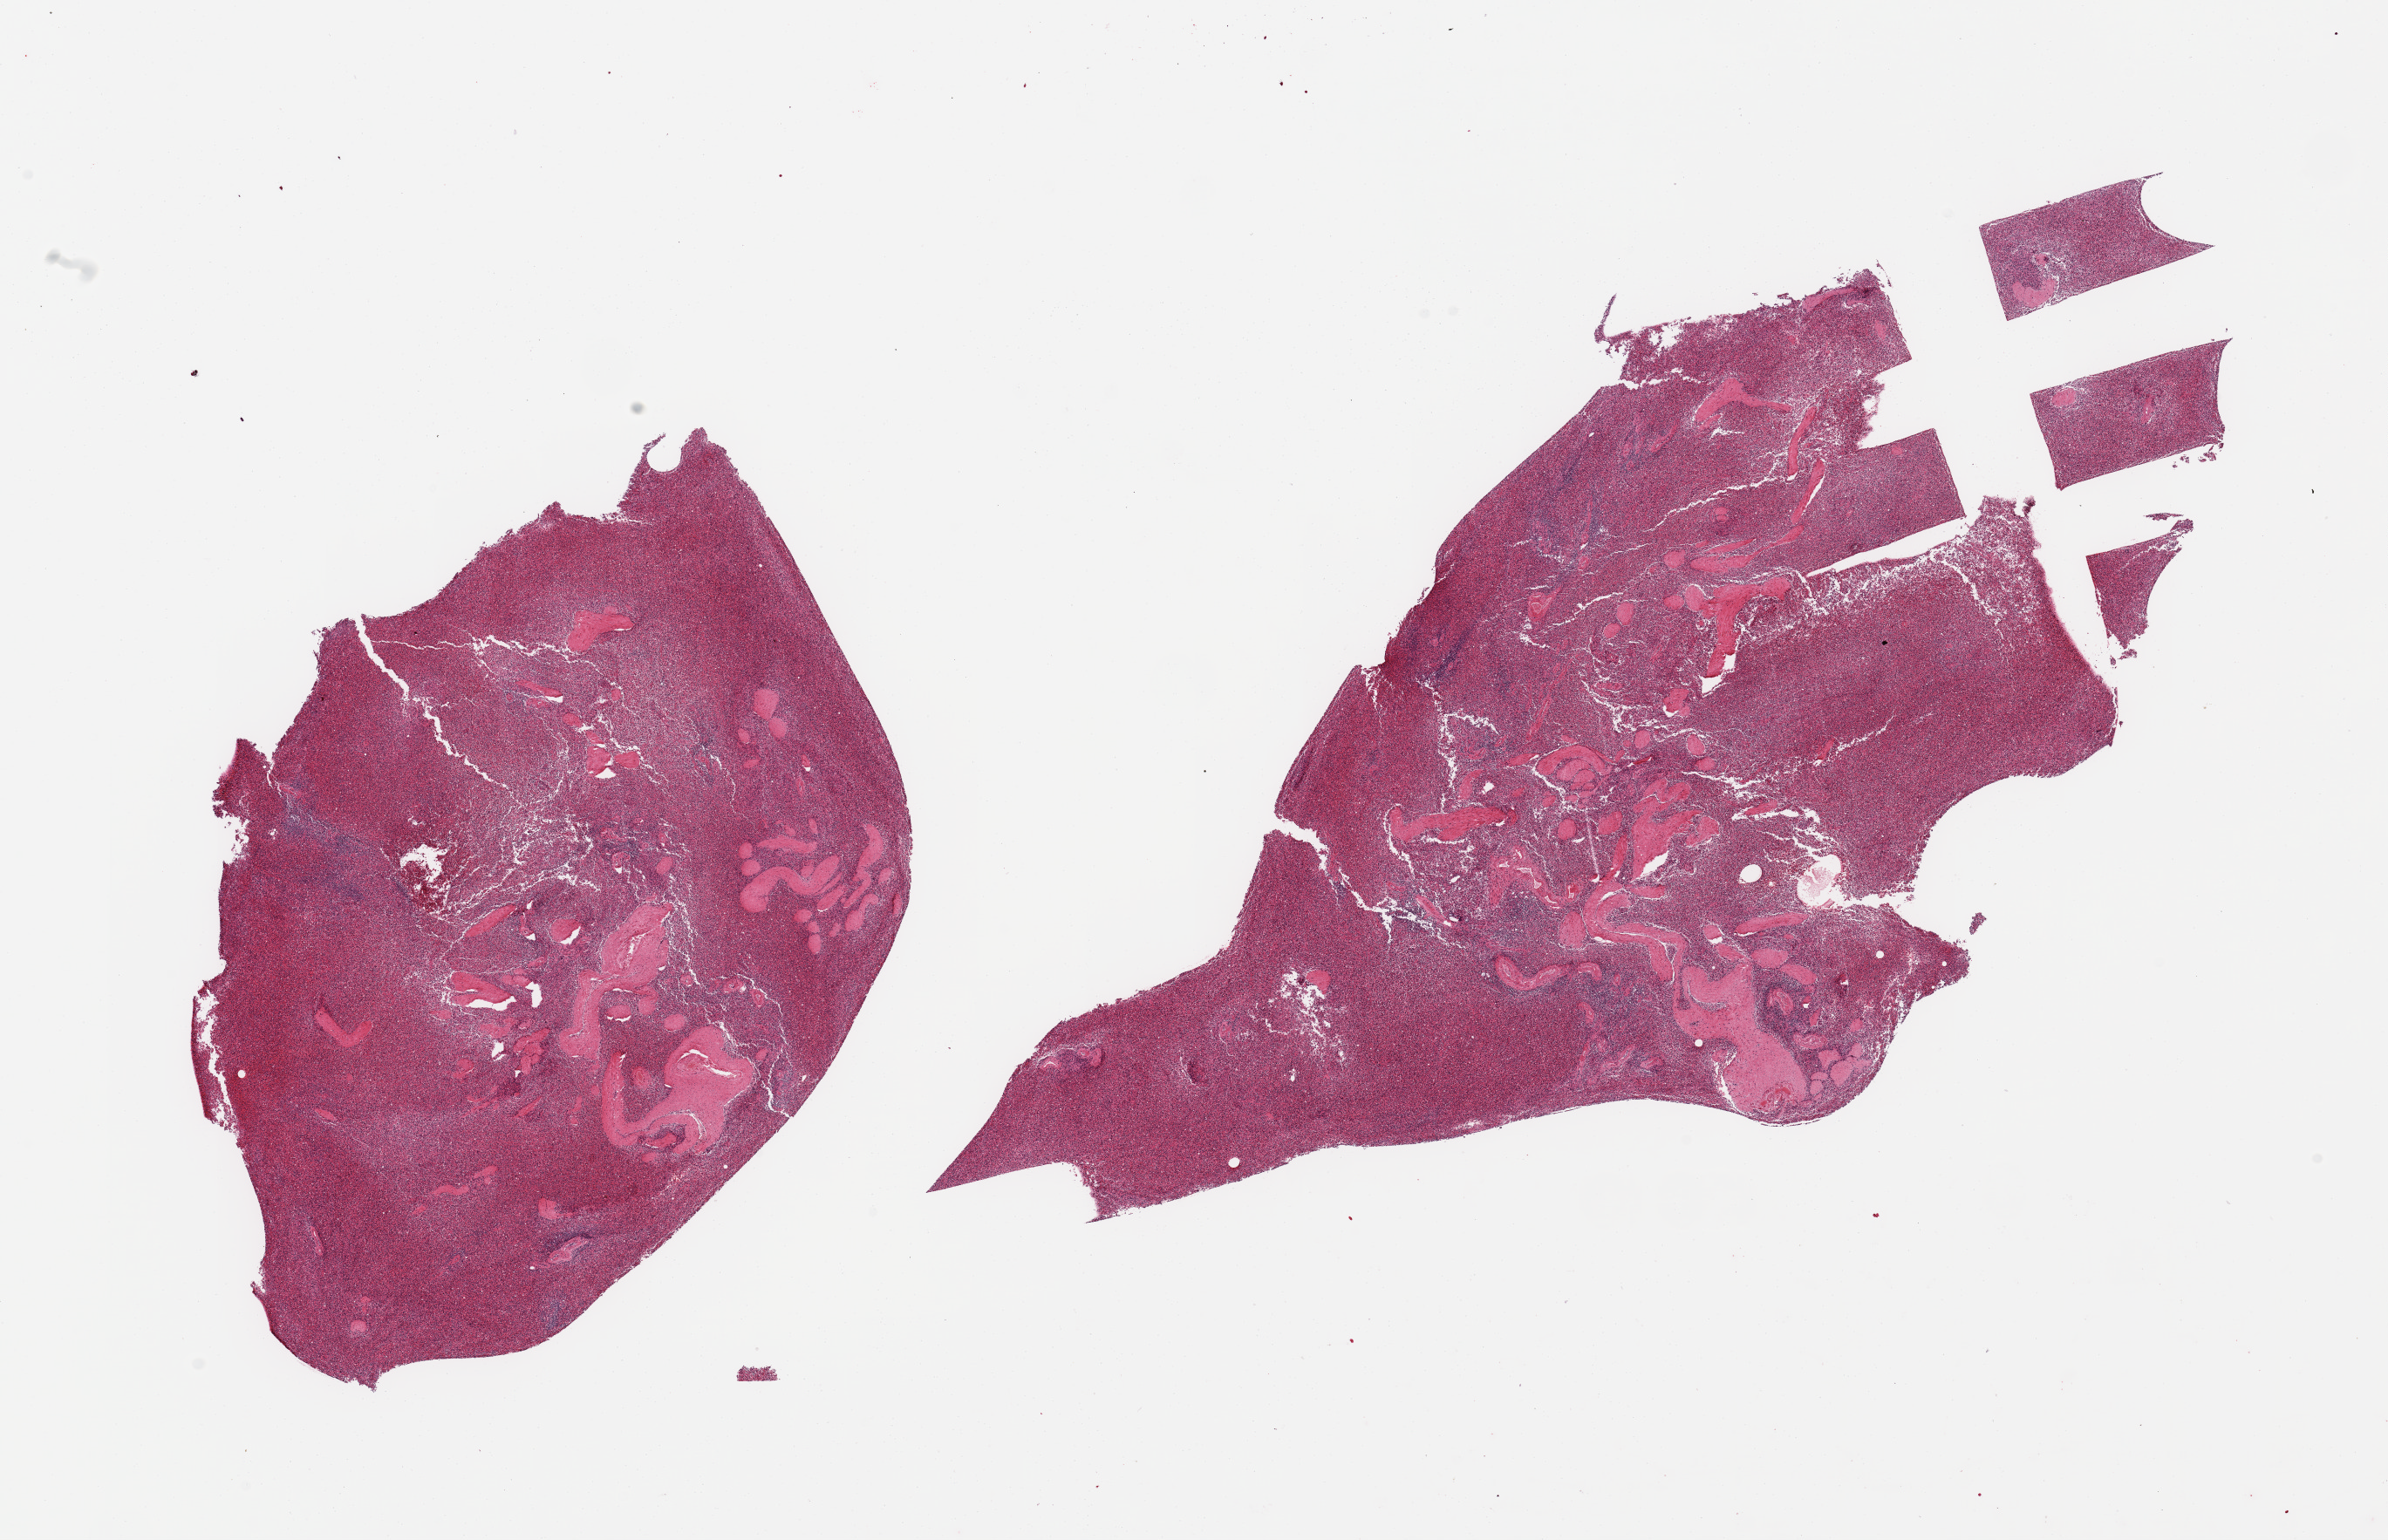
Whole-slide image, haematoxylin and eosin stain, brightfield — a low-resolution overview of the entire scanned area, about 21.7 x 14.0 mm; PAXgene-fixed paraffin-embedded (PFPE) section; section of spleen (target tissue); tissue donor sample. Male donor.
Review note (as recorded): 2 pieces; congestion.